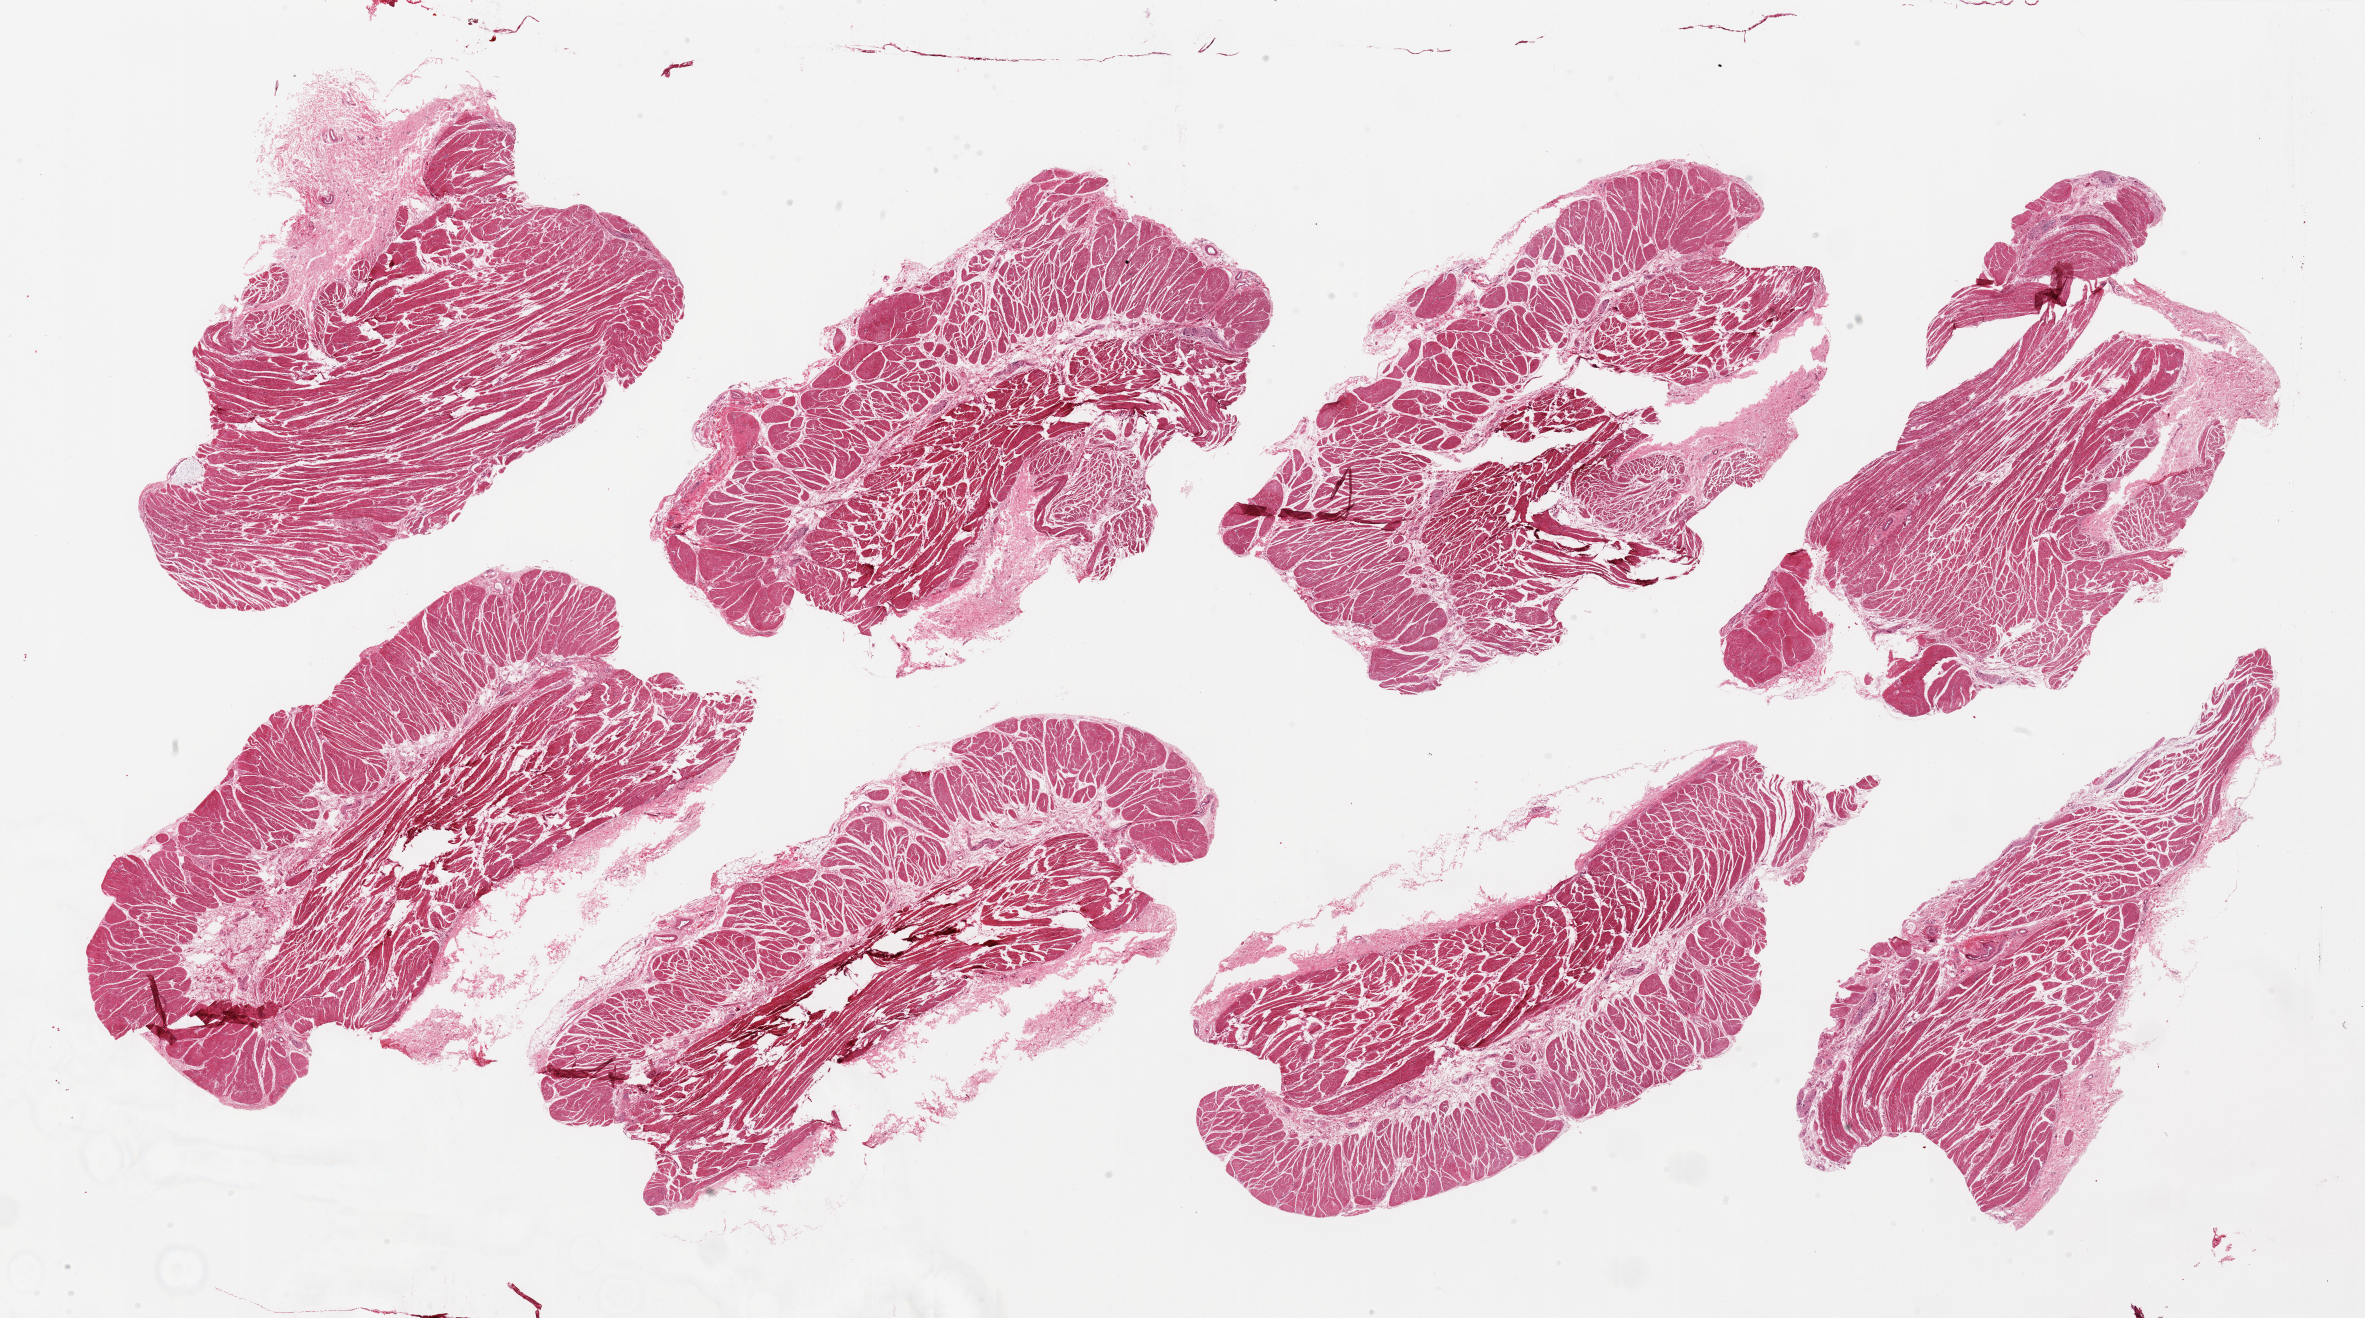
Digitized haematoxylin and eosin-stained section, shown as a low-resolution overview of the whole scanned area (about 37.4 x 20.8 mm, from a 20x scan); PAXgene-fixed, paraffin-embedded tissue; target tissue: esophageal muscle; tissue donor sample. Male donor.
Pathologist's review note for this sample: 8 pieces; some pieces are over-sized.